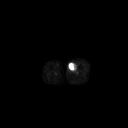
FDG PET of an extremity soft-tissue mass (from a PET/CT study), one axial slice. 128 × 128 image matrix, field of view 700 × 700 mm. Patient: male, 48 years. From the clinical record (not read from this slice): histological type: pleiomorphic leiomyosarcoma; grade: high; site of the primary tumour: left thigh.
Annotated regions visible in this slice (expert contour drawn on MRI and transferred to this co-registered scan by the dataset authors):
- gross tumour volume including surrounding oedema: bounding box (x1, y1, x2, y2) in pixels: (68, 63, 77, 72)
- gross tumour volume (mass): (68, 63, 77, 72)